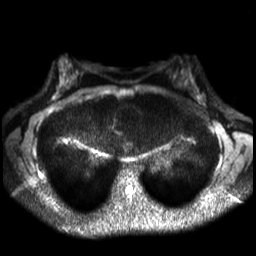
Breast MRI, one axial slice. Slice 20 of 30 in the series (ordered by position). Diffusion-weighted series; image 2 of 4 stored at this slice position (different b-values; order by instance number). 3 T. 4 mm slice thickness. 256 × 256 image matrix. Female patient.
Structures marked on this image (outlined manually by an expert reader):
- tumour on diffusion-weighted imaging: box from (x=194, y=96) to (x=202, y=103) px